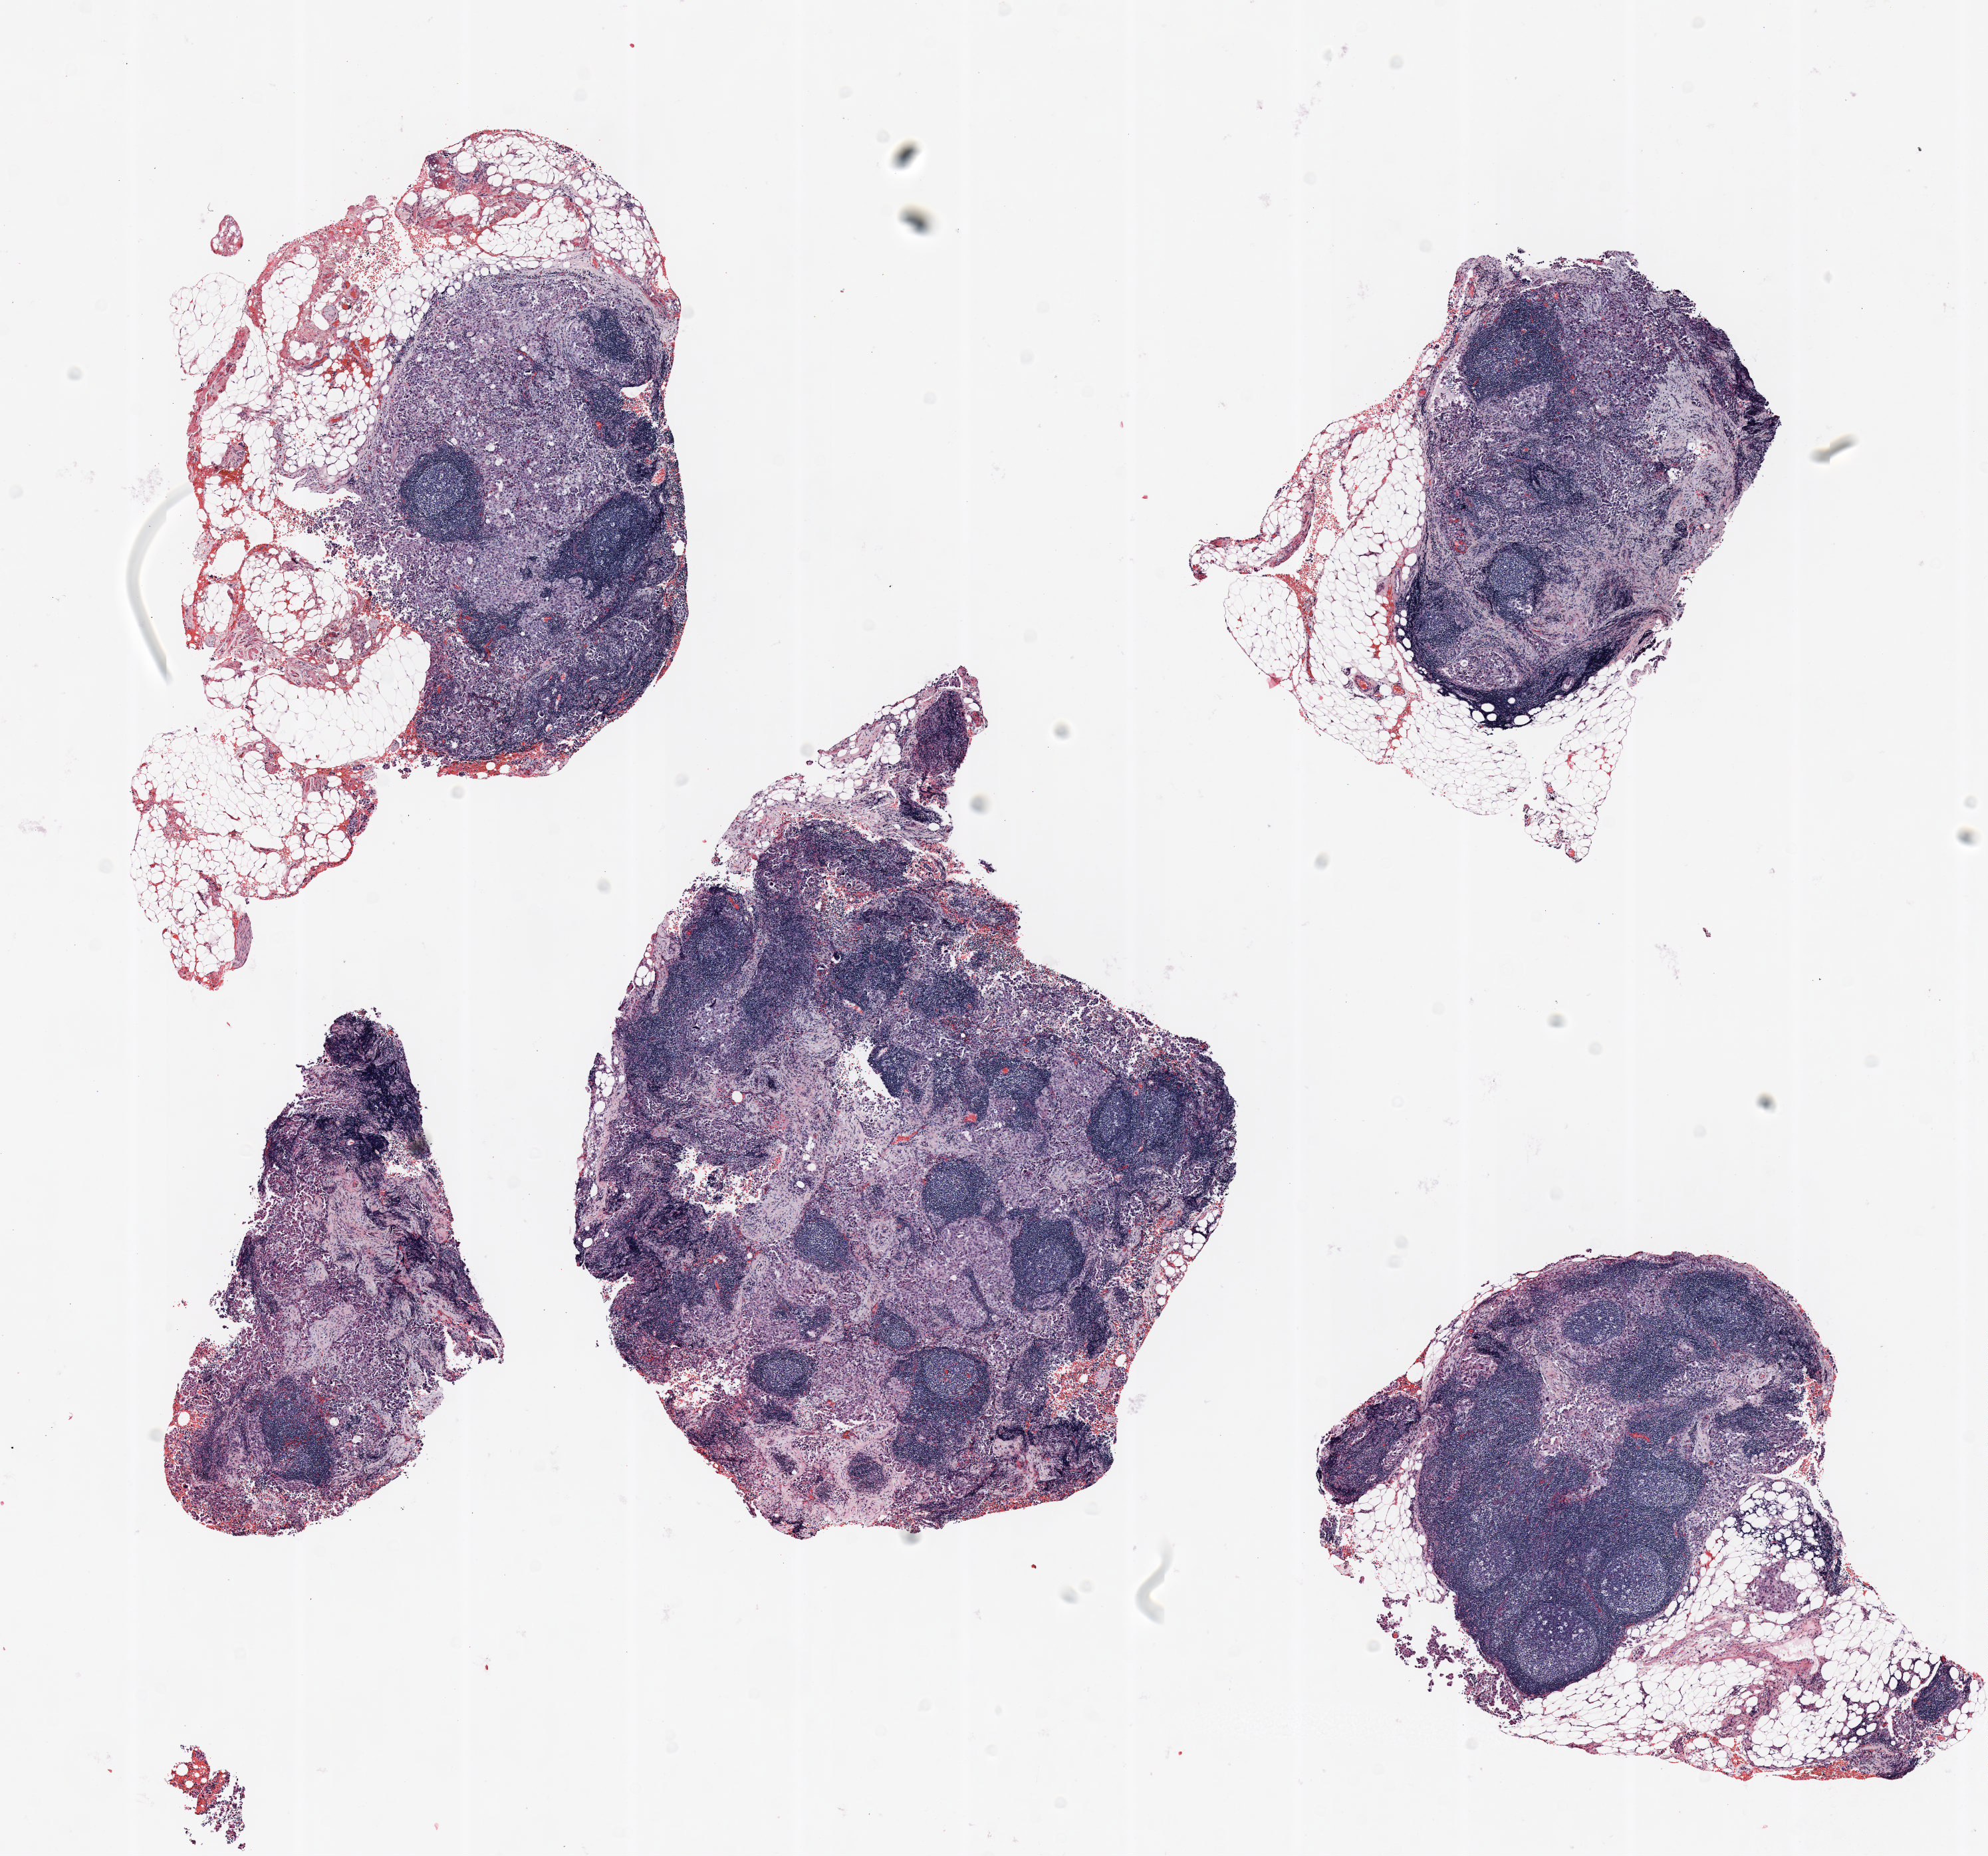
Whole-slide histology image, H&E — a low-resolution overview of the entire scanned area, about 12.0 x 11.2 mm (acquisition: 20x scan). Formalin-fixed paraffin-embedded (FFPE) section. Lung tissue. Male, age 64 at enrolment. Current smoker at enrolment. Grade: cannot be assessed (GX).
Primary tumour location (clinical record): right upper lobe. ICD-O-3 topography: upper lobe of lung (C34.1). Tumour size (pathology): 13 mm. Participant's lung-cancer diagnosis: Non-small cell carcinoma. Stage (AJCC 6th edition): IIIA.